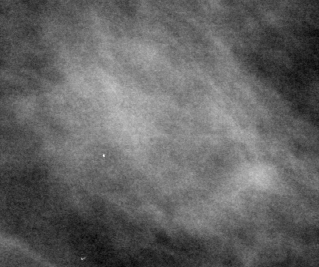
Crop from a digitized film mammogram around one marked abnormality, left breast, MLO view.
Marked abnormality: mass, shape oval, margins obscured / ill defined; BI-RADS assessment category 3; pathology result (as recorded, not read from the image): malignant.